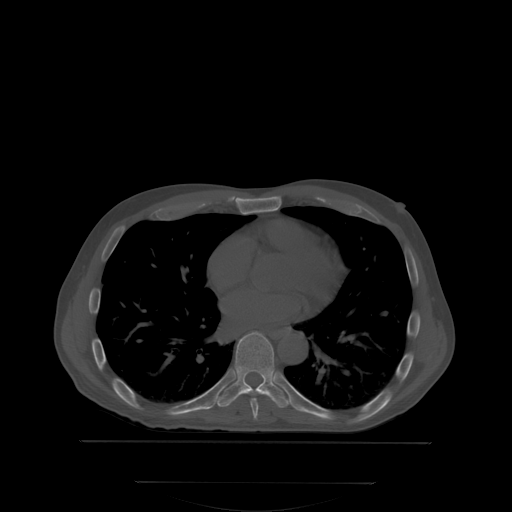
CT including the spine, one axial slice. Slice 218 of 350 in the series (ordered by position). Bone window (W 1800 / L 400 HU). 2.5 mm slice thickness. 512 × 512 image matrix. Male patient, age 58 years. From the clinical record (not read from this slice): primary cancer: prostate.
Outlined on this slice (semi-automatic segmentation, software-assisted and operator-edited):
- T7 vertebra: bounding box [x1, y1, x2, y2] px = [250, 398, 259, 418]
- T8 vertebra: [205, 331, 290, 407]